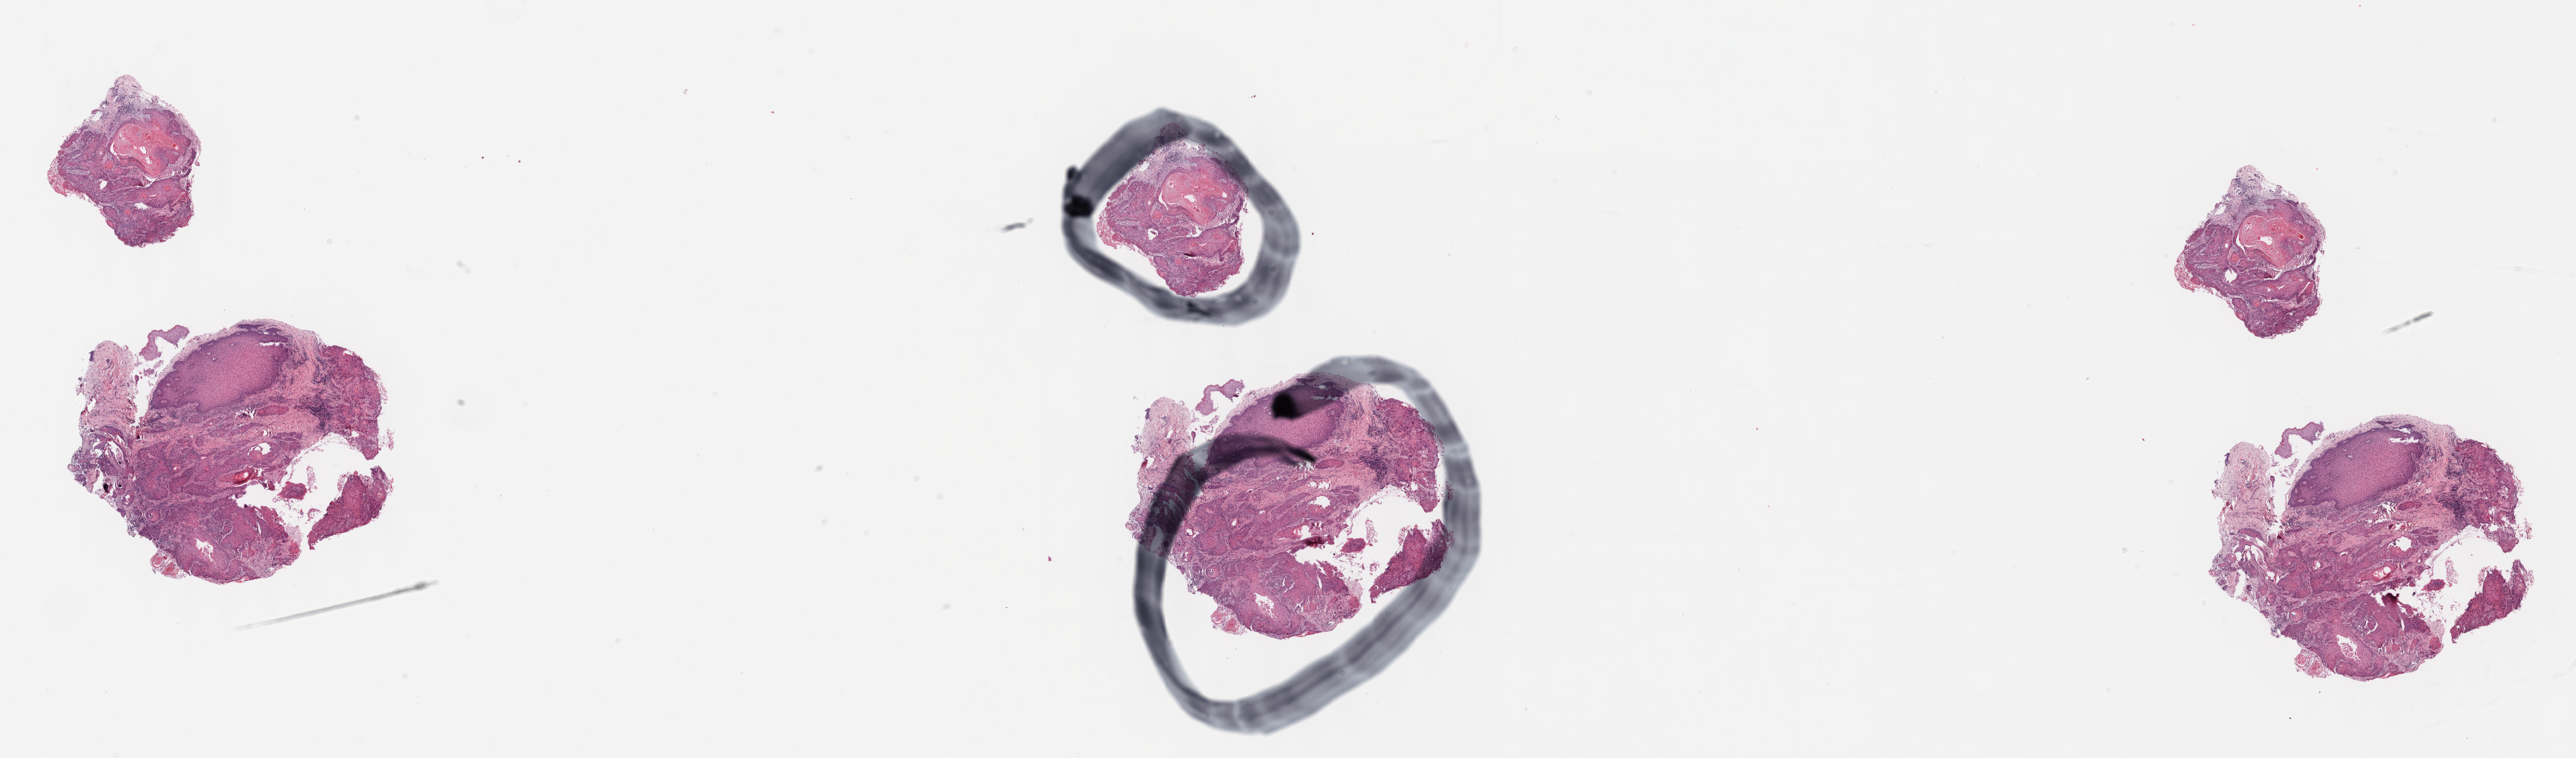
H&E-stained whole-slide image — low-resolution overview of the scanned area, about 31.2 x 9.2 mm (from a 40x scan). FFPE section. Head and neck, primary tumour sample. Female patient; age at initial diagnosis 52 years. Histologic grade: G2 (moderately differentiated).
Lymph nodes positive (case pathology): 0 of 19 examined. Pathologic diagnosis: Squamous cell carcinoma, NOS (tongue, NOS). Laterality: right.